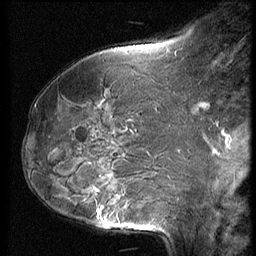
Breast MRI (dynamic contrast-enhanced), one sagittal slice; slice 24 of 62 in the series (ordered by position); 3 images stored at this slice position (order not interpretable as contrast timing); 1.5 T; TE 4.2 ms, TR 9 ms; 2.5 mm slice thickness; 256 × 256 image matrix, field of view 180 × 180 mm. Female patient, age 50 years. Case-level facts recorded for this patient, not image findings: setting: breast cancer imaged before/during neoadjuvant chemotherapy; receptor status: HR-positive, HER2-negative.
Annotated regions visible in this slice (semi-automatic segmentation, software-assisted and operator-edited):
- analysis volume of interest (the breast-tissue region the enhancement analysis was run in; not a lesion): box from (x=59, y=125) to (x=139, y=234) px
- tumour enhancement mask (voxels above the 140 % enhancement threshold inside the analysis volume of interest): (x=98, y=209)–(x=102, y=218)